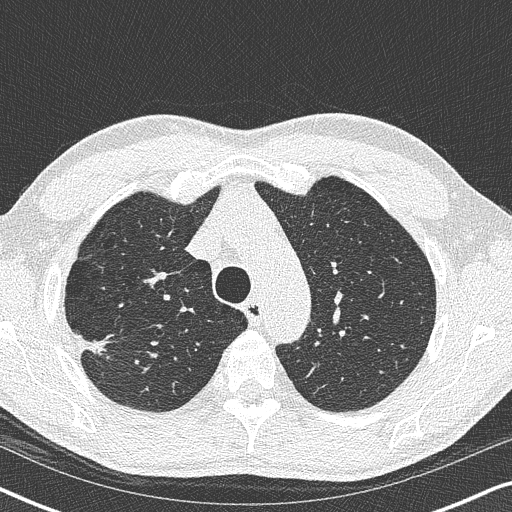
Low-dose screening chest CT, one axial slice; position 281 of 356 along the scan axis; 120 kVp; lung window (W 1500 / L -600 HU); 1 mm slice thickness; 512 × 512 image matrix, field of view 330 × 330 mm.
Outlined on this slice (outlined manually by an expert reader):
- lesion 1 (tumor, upper lobe of right lung): bounding box <80,337,107,353> (left, top, right, bottom; pixels)